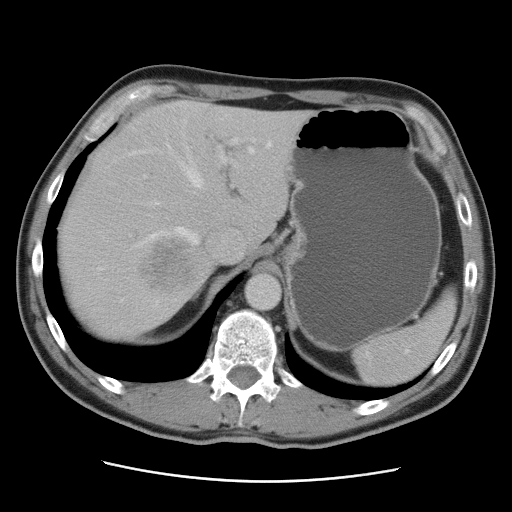
Contrast-enhanced abdominal CT, one axial slice; slice 67 of 89 in the series (ordered by position); 120 kVp; intravenous contrast given; soft-tissue window (W 400 / L 40 HU); 5 mm slice thickness; 512 × 512 image matrix, field of view 366 × 366 mm. Male patient, age 59 years. From the clinical record (not read from this slice): diagnosis: colorectal cancer liver metastases, imaged before liver resection; multiple liver metastases: yes; largest metastasis: 0.6 cm; chemotherapy before resection: no.
Structures marked on this image (expert manual segmentation):
- hepatic veins: bounding box (x1, y1, x2, y2) in pixels: (98, 143, 271, 271)
- liver: (58, 98, 311, 341)
- planned liver remnant (the part of the liver to remain after resection): (103, 99, 311, 249)
- portal vein (with intrahepatic branches): (144, 138, 256, 178)
- liver metastasis: (142, 241, 193, 289)